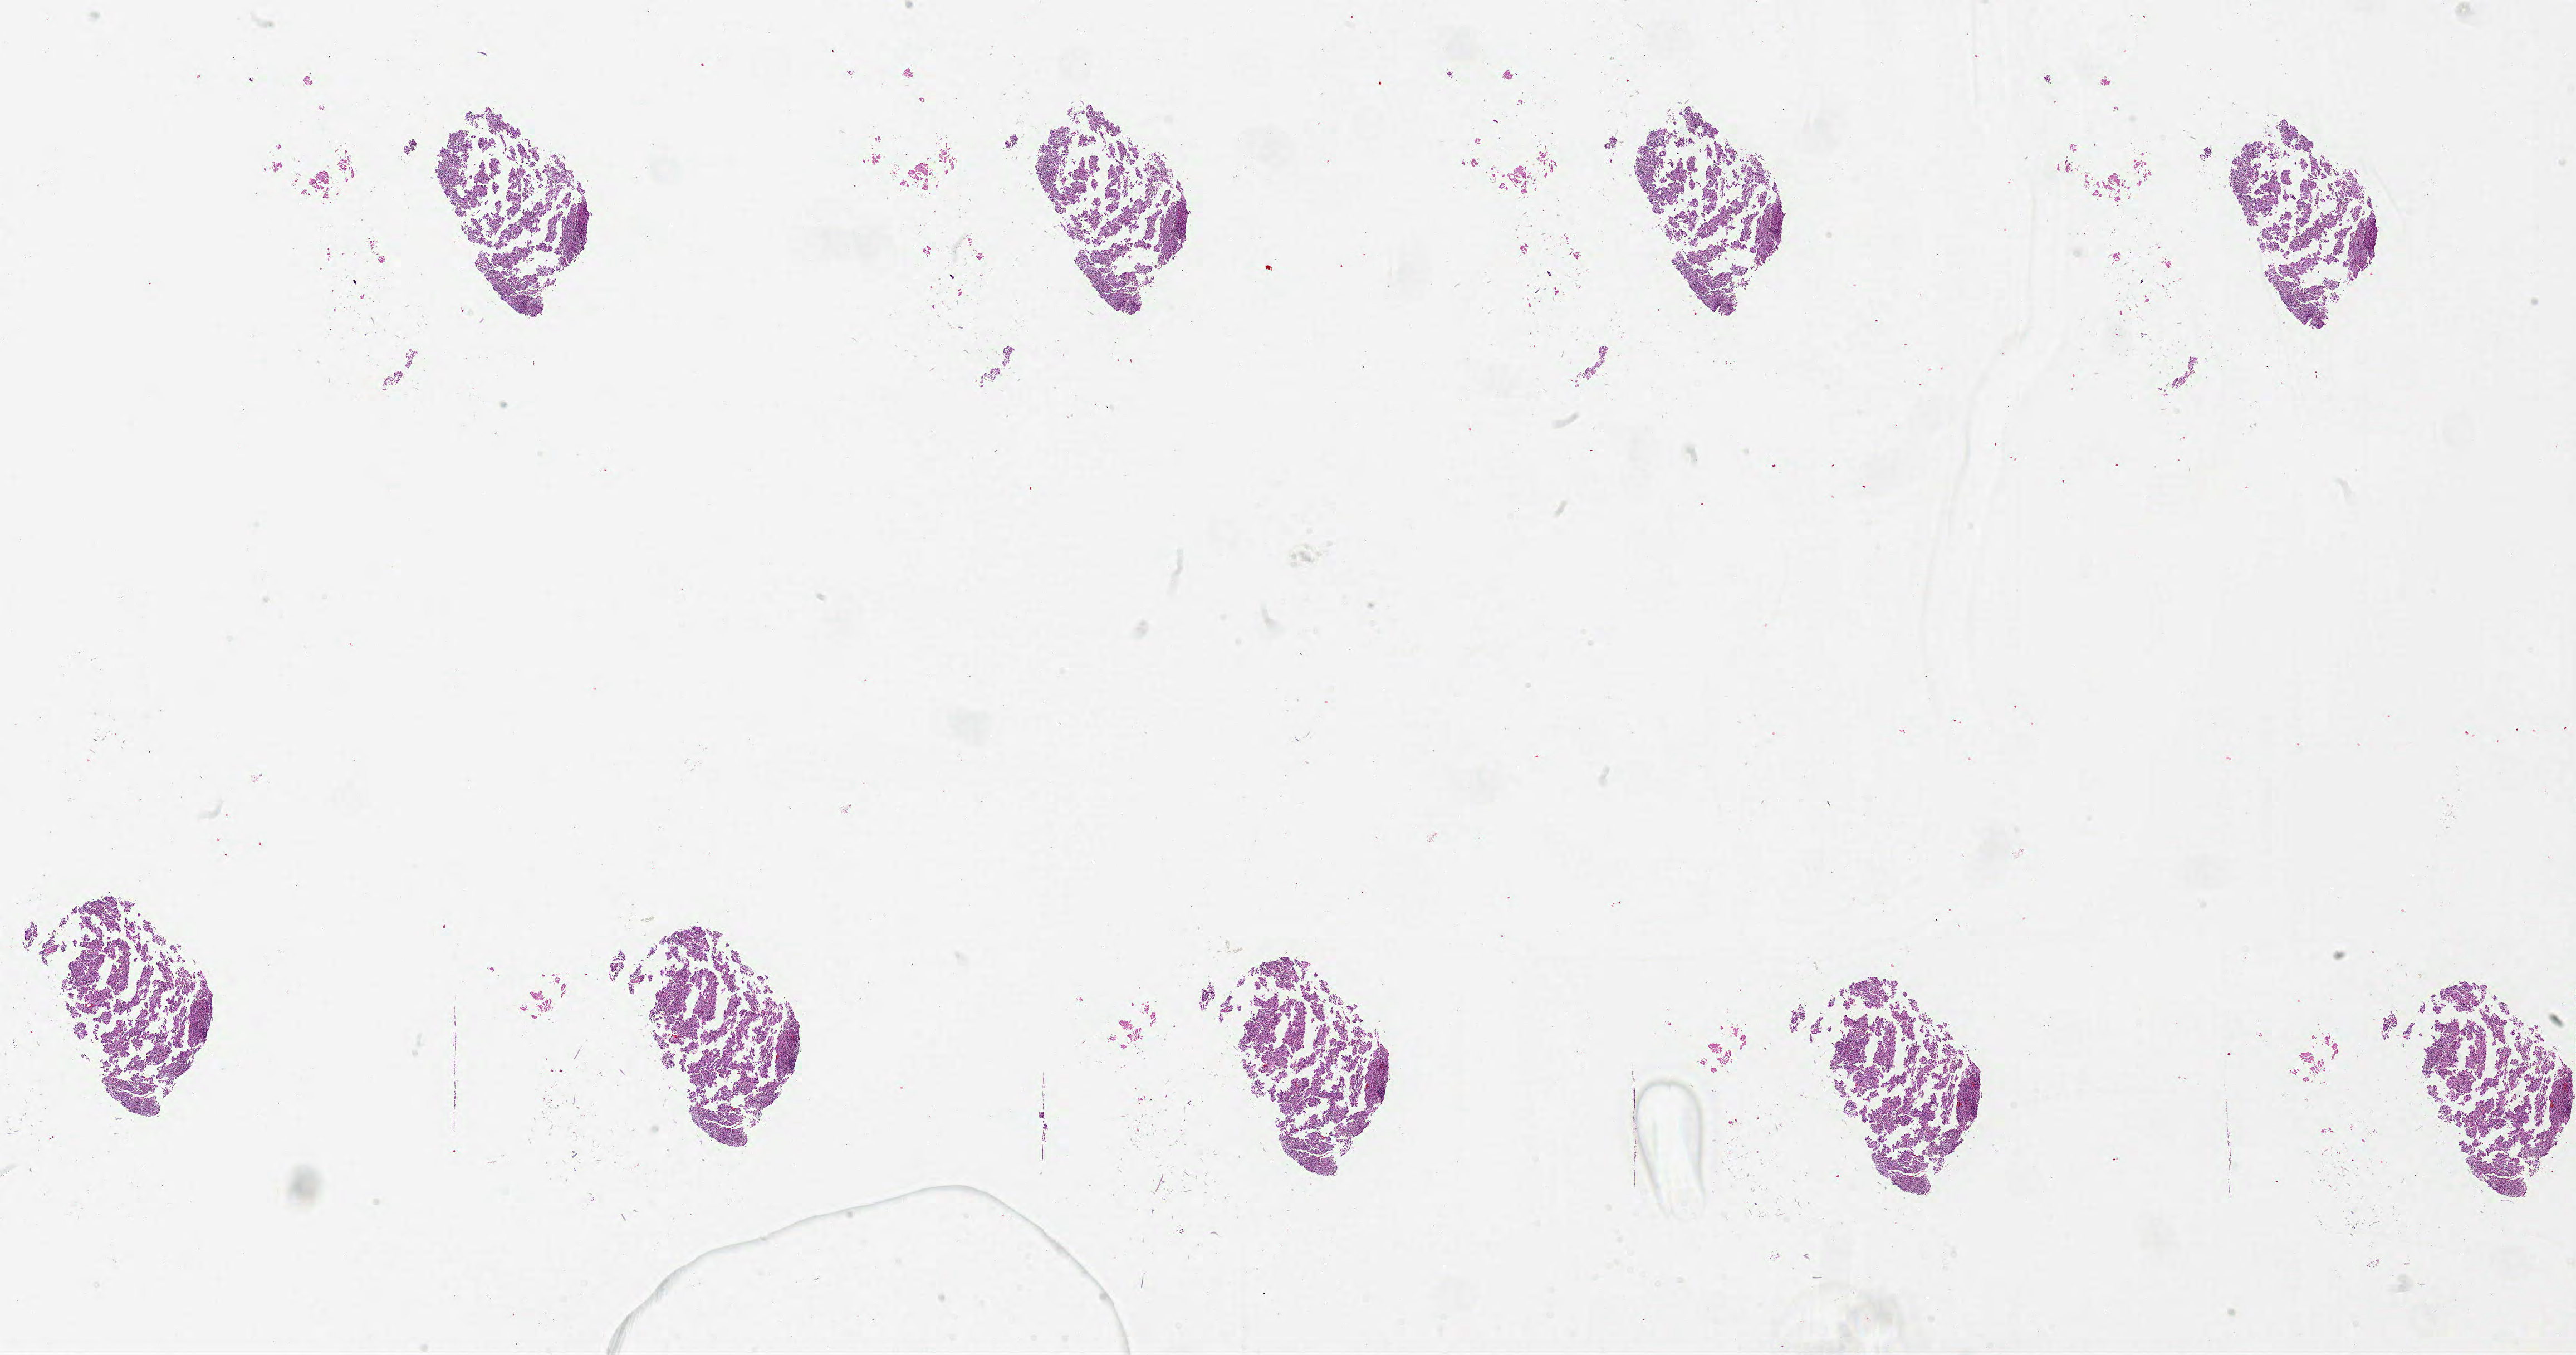
Hematoxylin and eosin (H&E) stained whole-slide image — a low-resolution overview of the entire scanned area, about 37.0 x 19.4 mm, formalin-fixed paraffin-embedded (FFPE) diagnostic section, primary tumour sample from the brain. Patient: male, age at initial diagnosis 52 years.
- histologic diagnosis: Glioblastoma